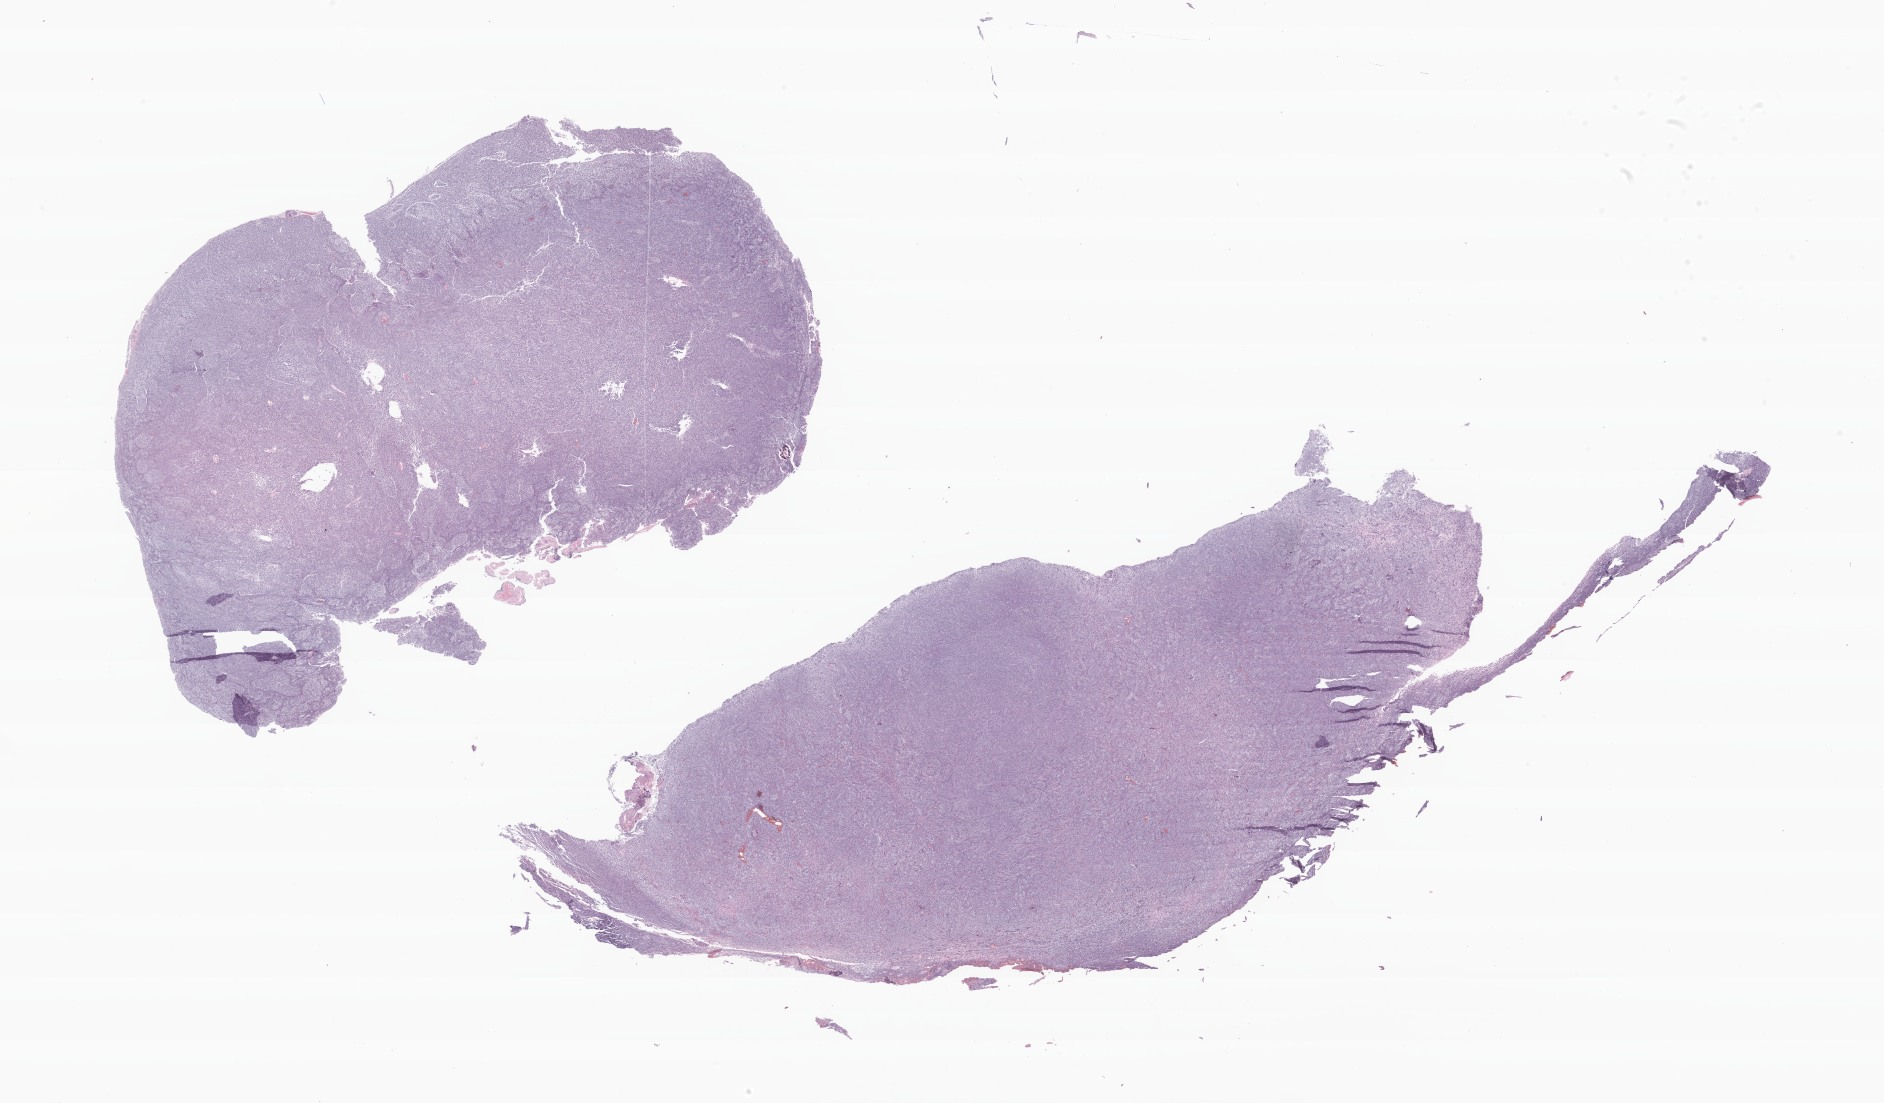
Digitized hematoxylin and eosin (H&E)-stained section of tumor tissue from the brain — shown as a low-resolution overview of the whole scanned area (about 31.7 x 18.6 mm). Formalin-fixed, paraffin-embedded (FFPE) tissue. Male patient, age 216 months.
Diagnosis (ICD-O-3 morphology term): Desmoplastic nodular medulloblastoma.